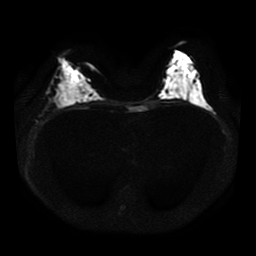
Breast MRI, one axial slice. Slice 21 of 41 in the series (ordered by position). Diffusion-weighted series; image 2 of 4 stored at this slice position (different b-values; order by instance number). 1.5 T. 5 mm slice thickness. 256 × 256 image matrix. Female patient.
Structures marked on this image (outlined manually by an expert reader):
- tumour on diffusion-weighted imaging: box from (x=59, y=99) to (x=70, y=107) px